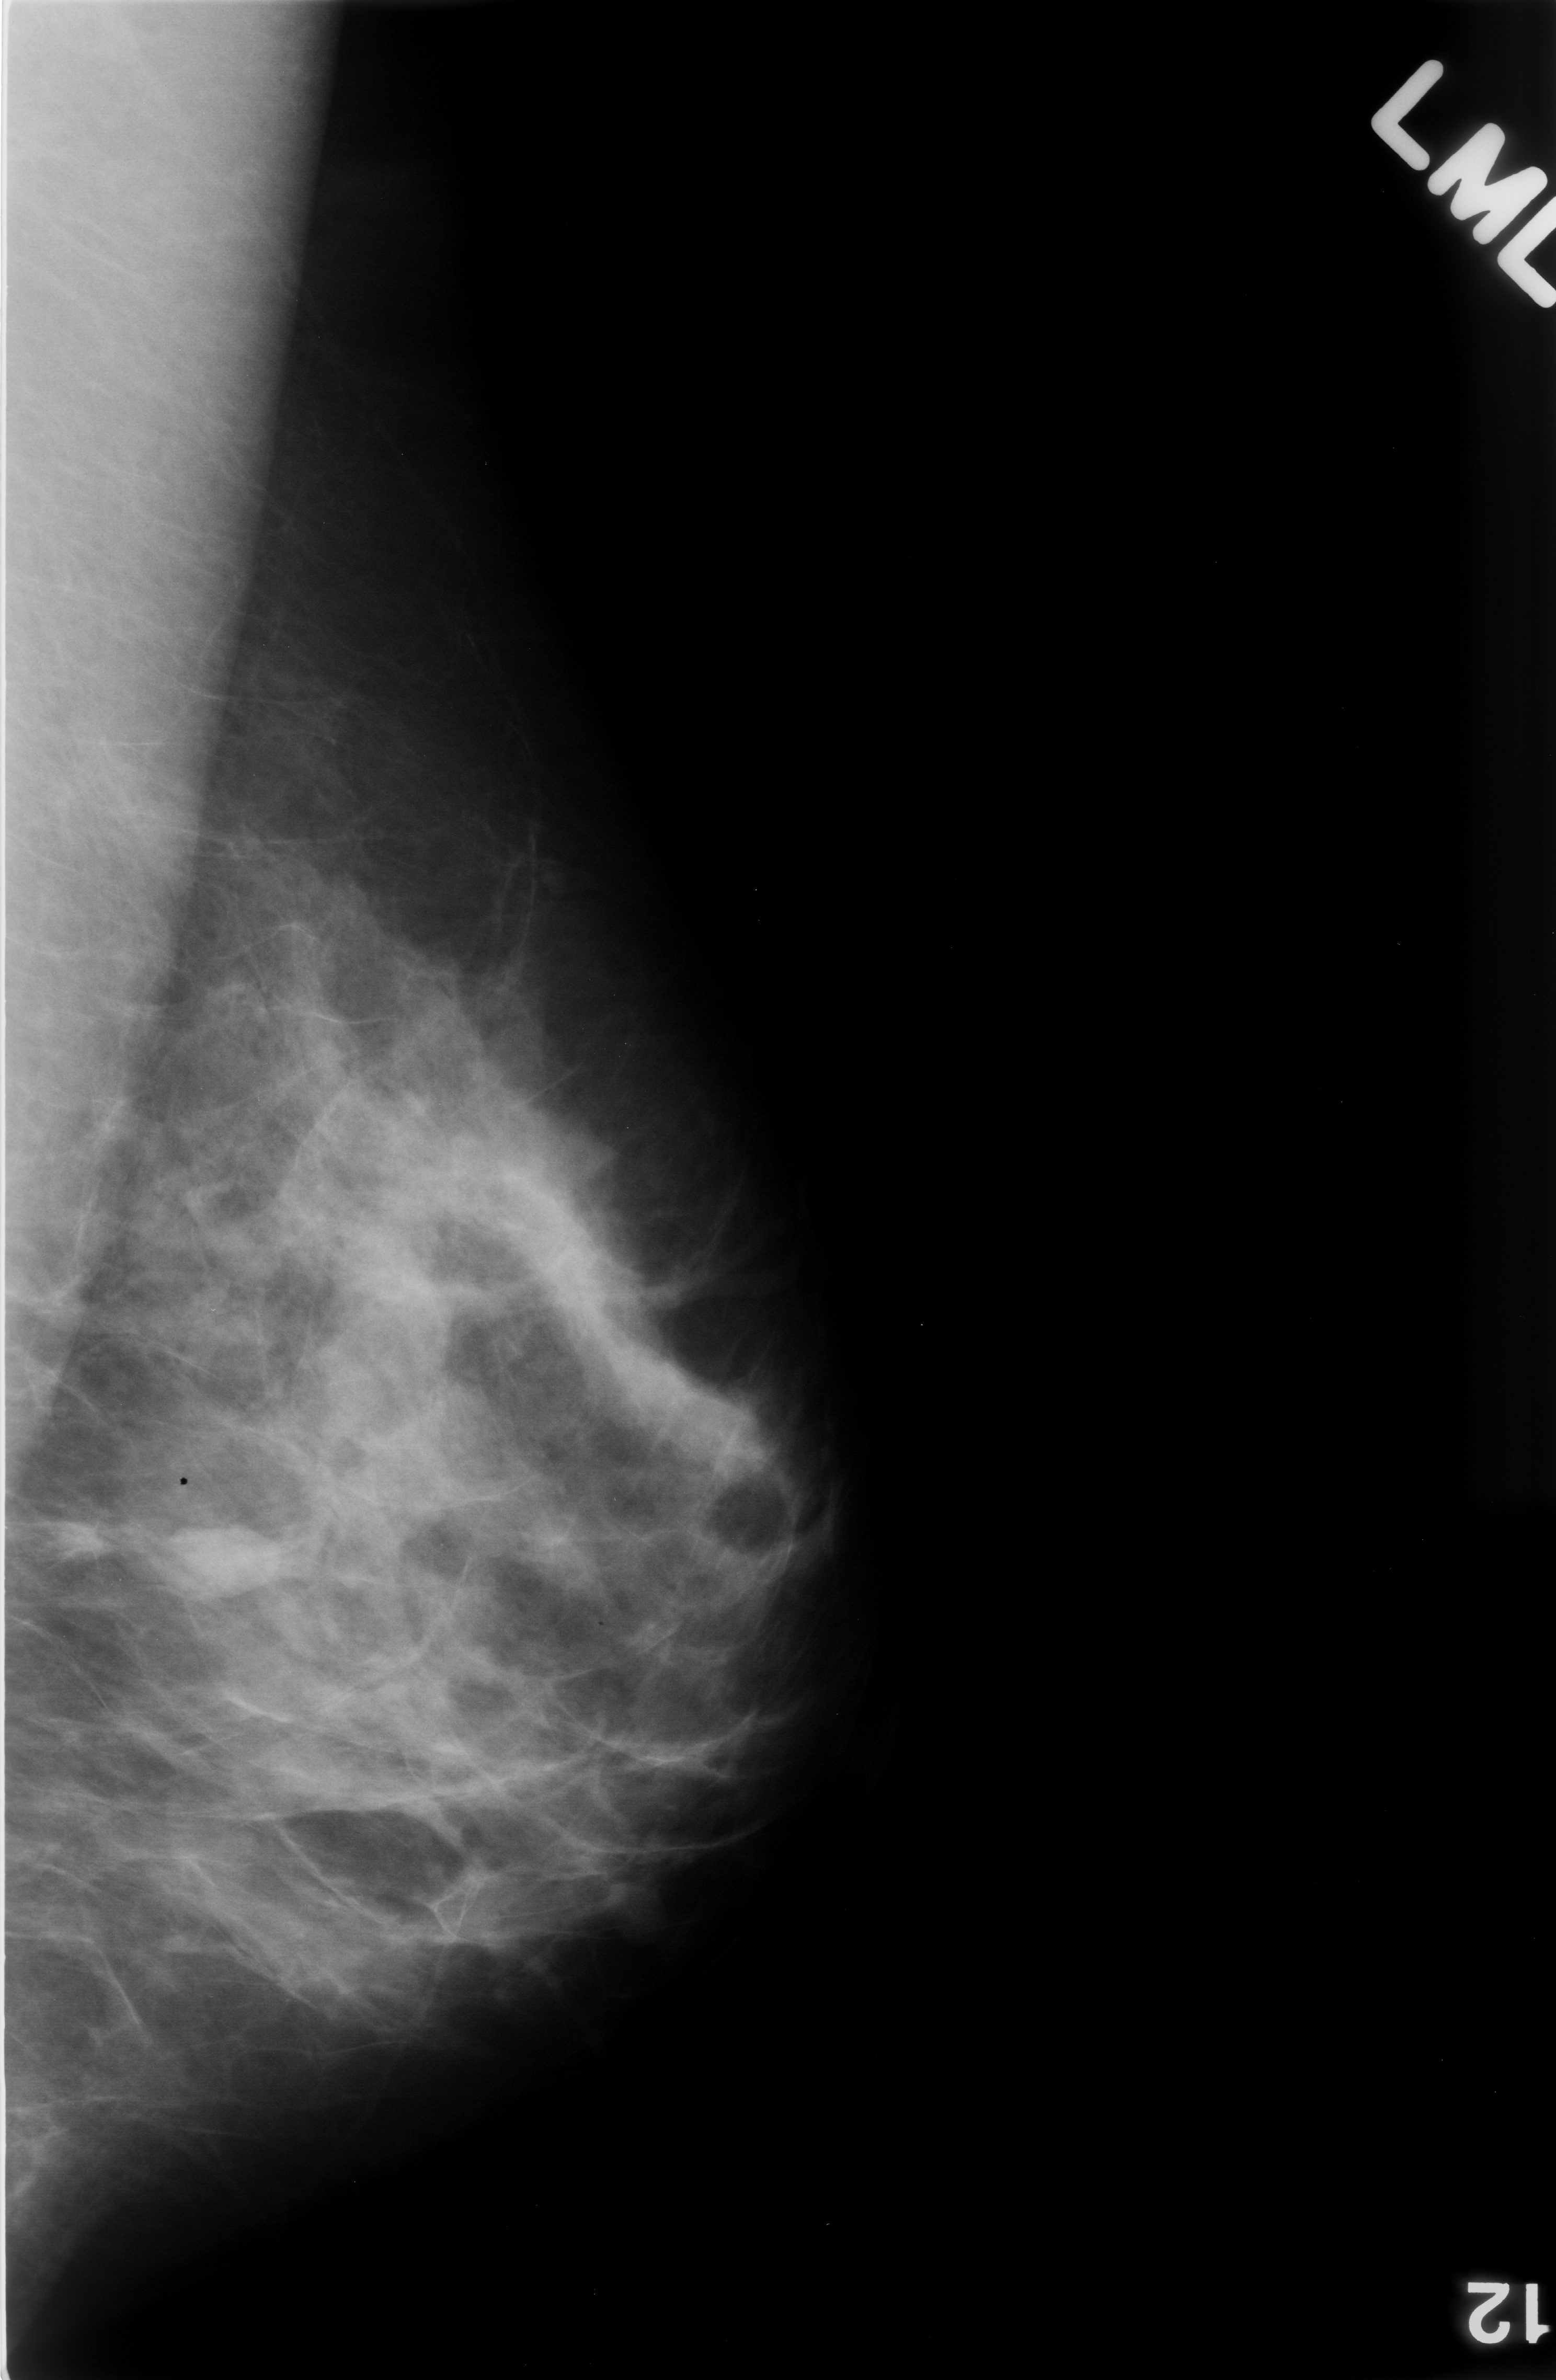
Mammogram (digitized film), left breast, mediolateral oblique (MLO) view, breast composition: scattered fibroglandular densities (BI-RADS density category 2 of 4).
Abnormality record for this image: mass, shape oval, margins circumscribed; BI-RADS assessment category 3; pathology (as recorded): benign.